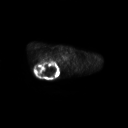
FDG PET of an extremity soft-tissue mass (from a PET/CT study), one axial slice; position 208 of 267 along the scan axis; 3.27 mm slice thickness; 128 × 128 image matrix, field of view 700 × 700 mm. Male patient, age 61 years. Case-level facts recorded for this patient, not image findings: histological type: pleiomorphic spindle cell undifferentiated; grade: high; site of the primary tumour: right parascapusular.
Structures marked on this image (expert contour drawn on MRI and transferred to this co-registered scan by the dataset authors):
- gross tumour volume including surrounding oedema: bounding box <34,60,60,77> (left, top, right, bottom; pixels)
- gross tumour volume (mass): <34,61,59,76>